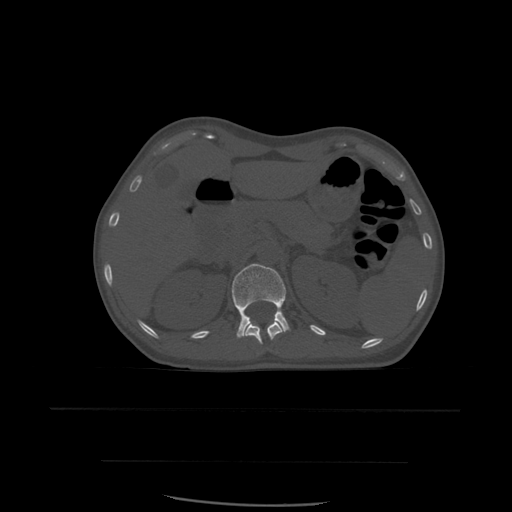
CT including the spine, one axial slice. Slice 260 of 574 in the series (ordered by position). Bone window (W 1800 / L 400 HU). 512 × 512 image matrix. Patient age 48 years. Case-level facts recorded for this patient, not image findings: primary cancer: lung.
Outlined on this slice (semi-automatically segmented with operator editing):
- L1 vertebra: bounding box <232,264,290,338> (left, top, right, bottom; pixels)
- T12 vertebra: <245,322,283,345>